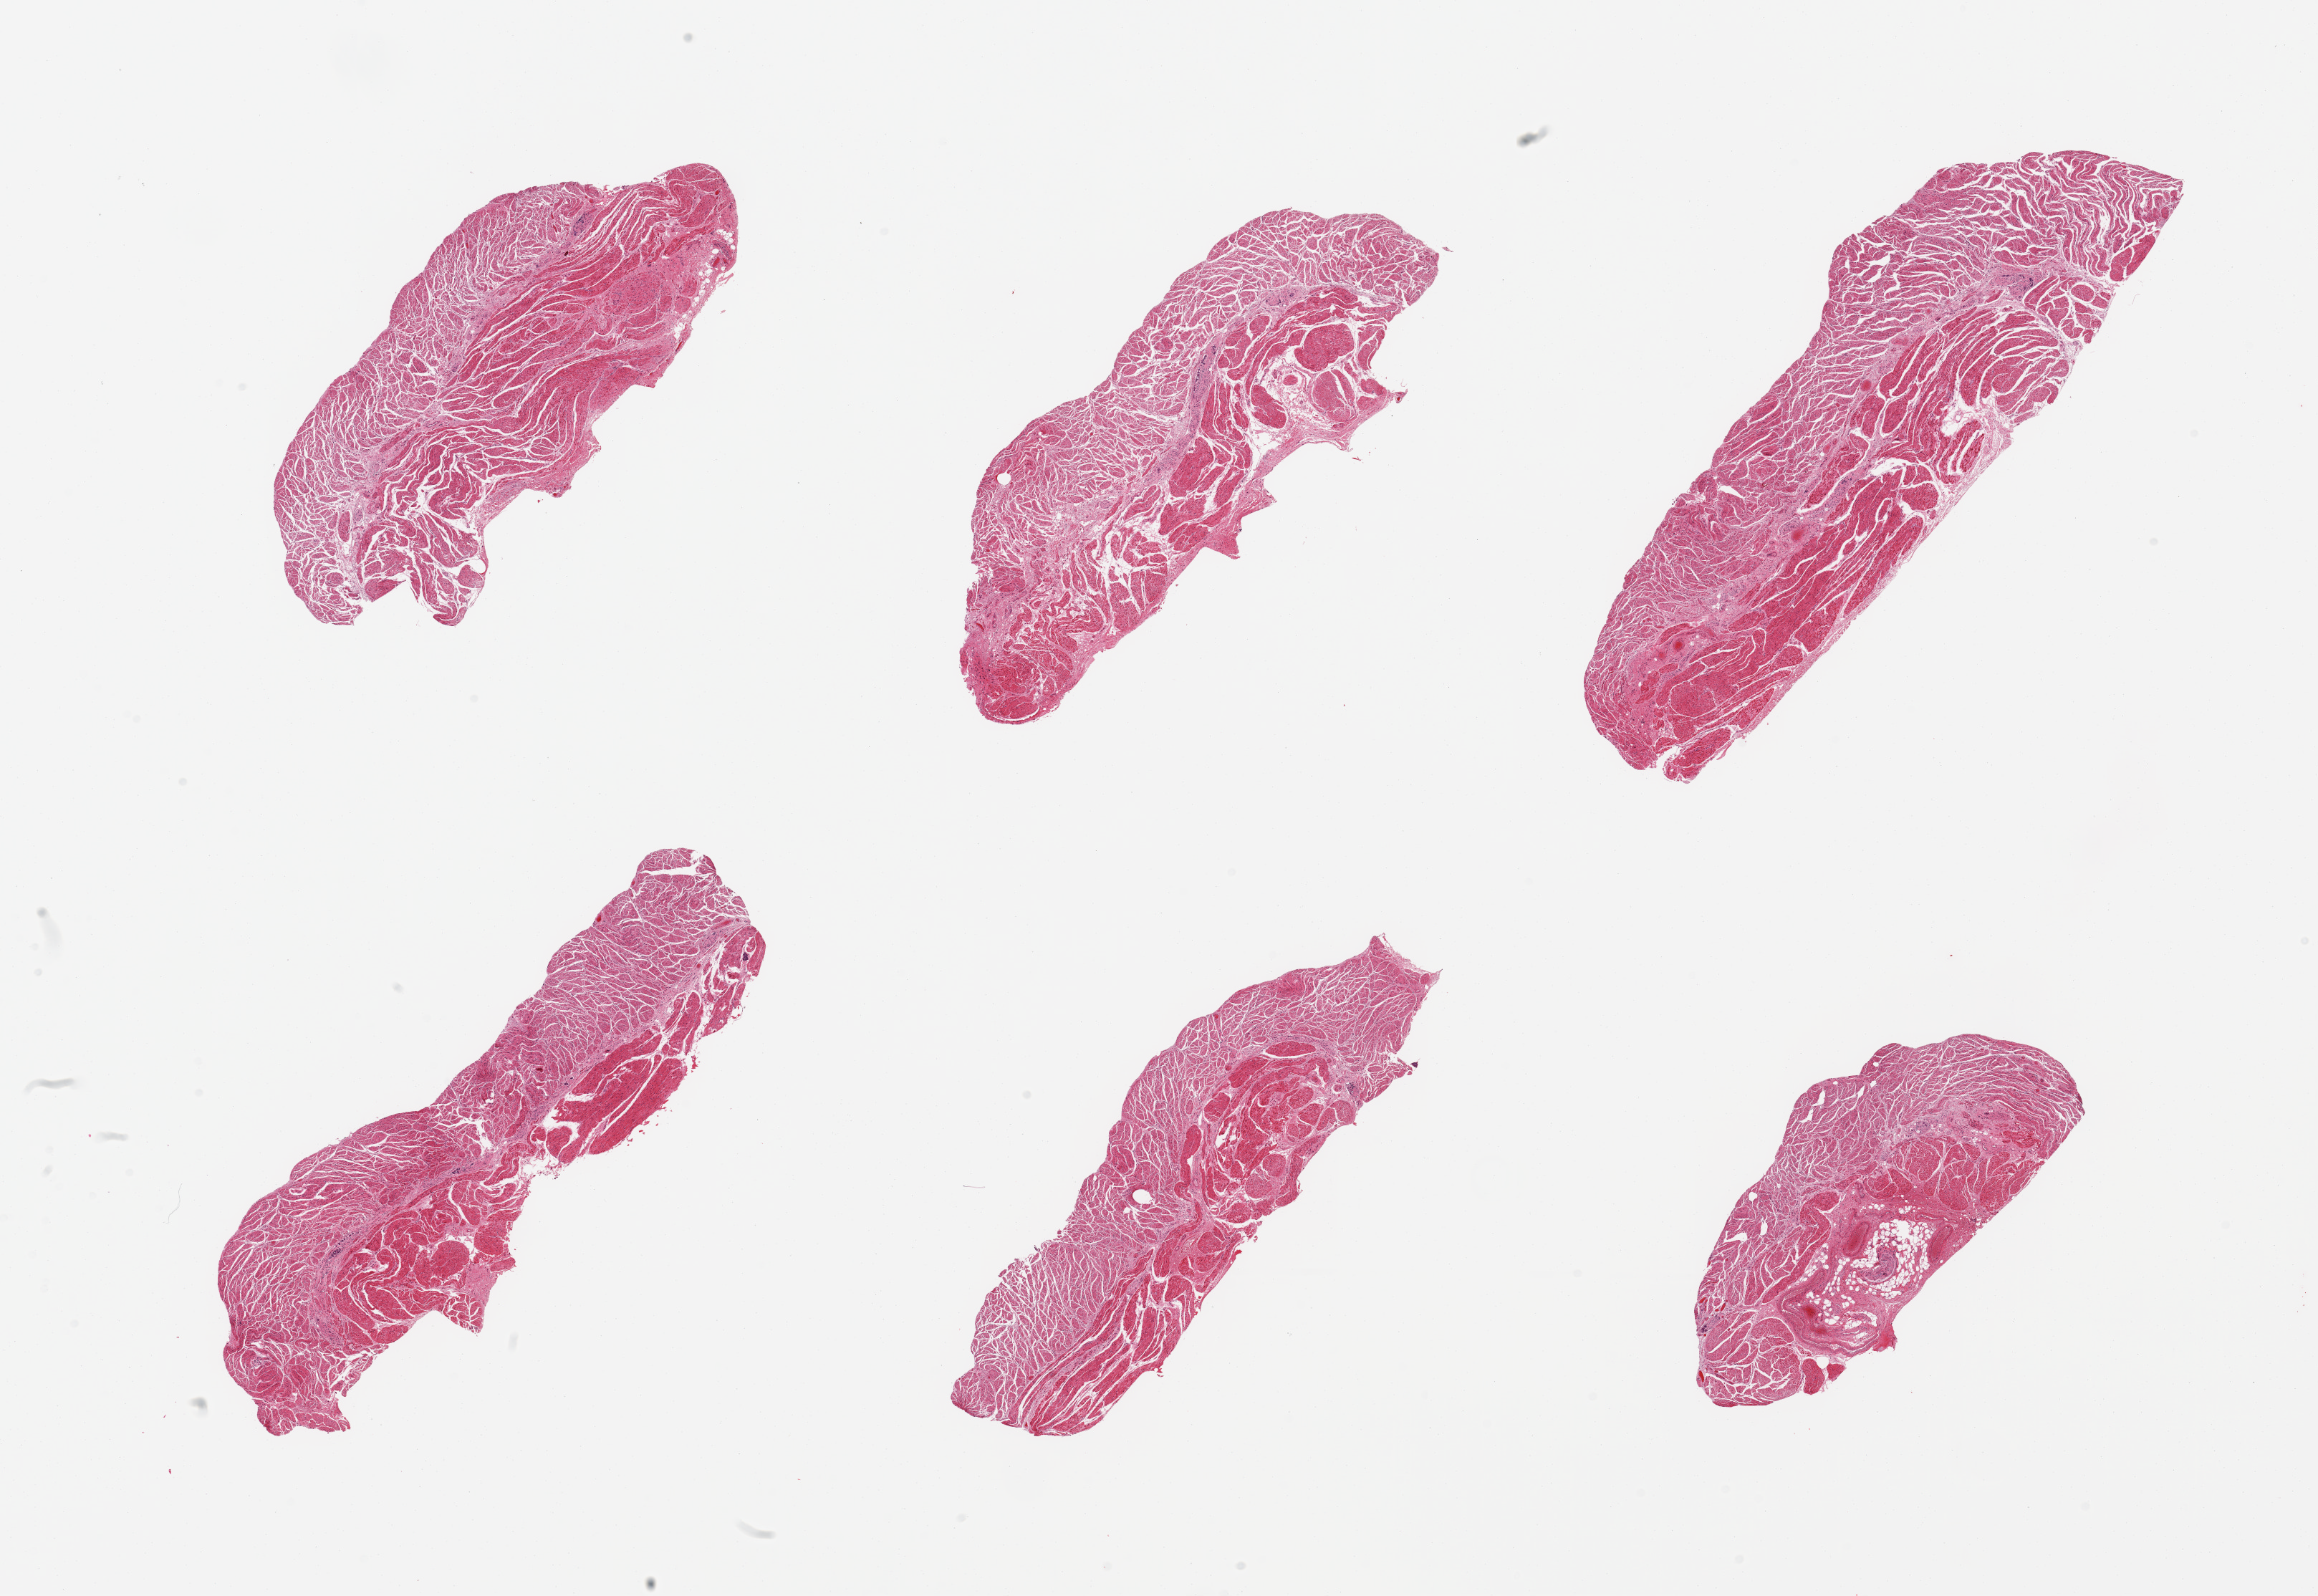
H&E whole-slide image — shown as a low-resolution overview of the whole scanned area (about 25.6 x 17.6 mm, slide scanned at 20x); PAXgene-fixed, paraffin-embedded tissue; section of esophageal muscle (target tissue); donor tissue sample. Male donor.
Pathologist's review note for this sample: 6 pieces; well dissected muscle.